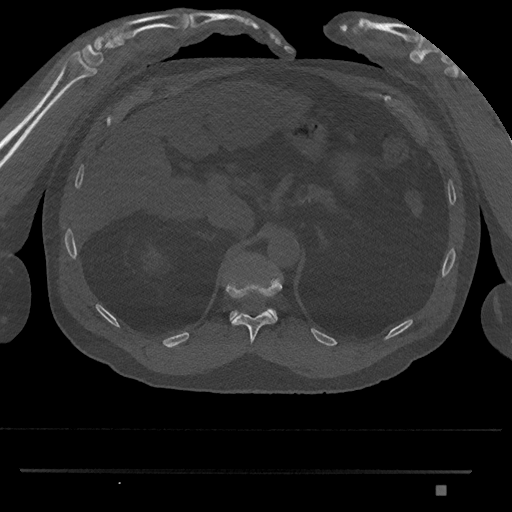
CT including the spine, one axial slice; reconstruction kernel Br40s/3; bone window (W 1800 / L 400 HU); 0.5 mm slice thickness; 512 × 512 image matrix. Patient: male, 65 years. Case-level facts recorded for this patient, not image findings: primary cancer: prostate.
Structures marked on this image (semi-automatically segmented with operator editing):
- T11 vertebra: bounding box (x1, y1, x2, y2) in pixels: (226, 278, 282, 345)
- T12 vertebra: (229, 308, 278, 321)